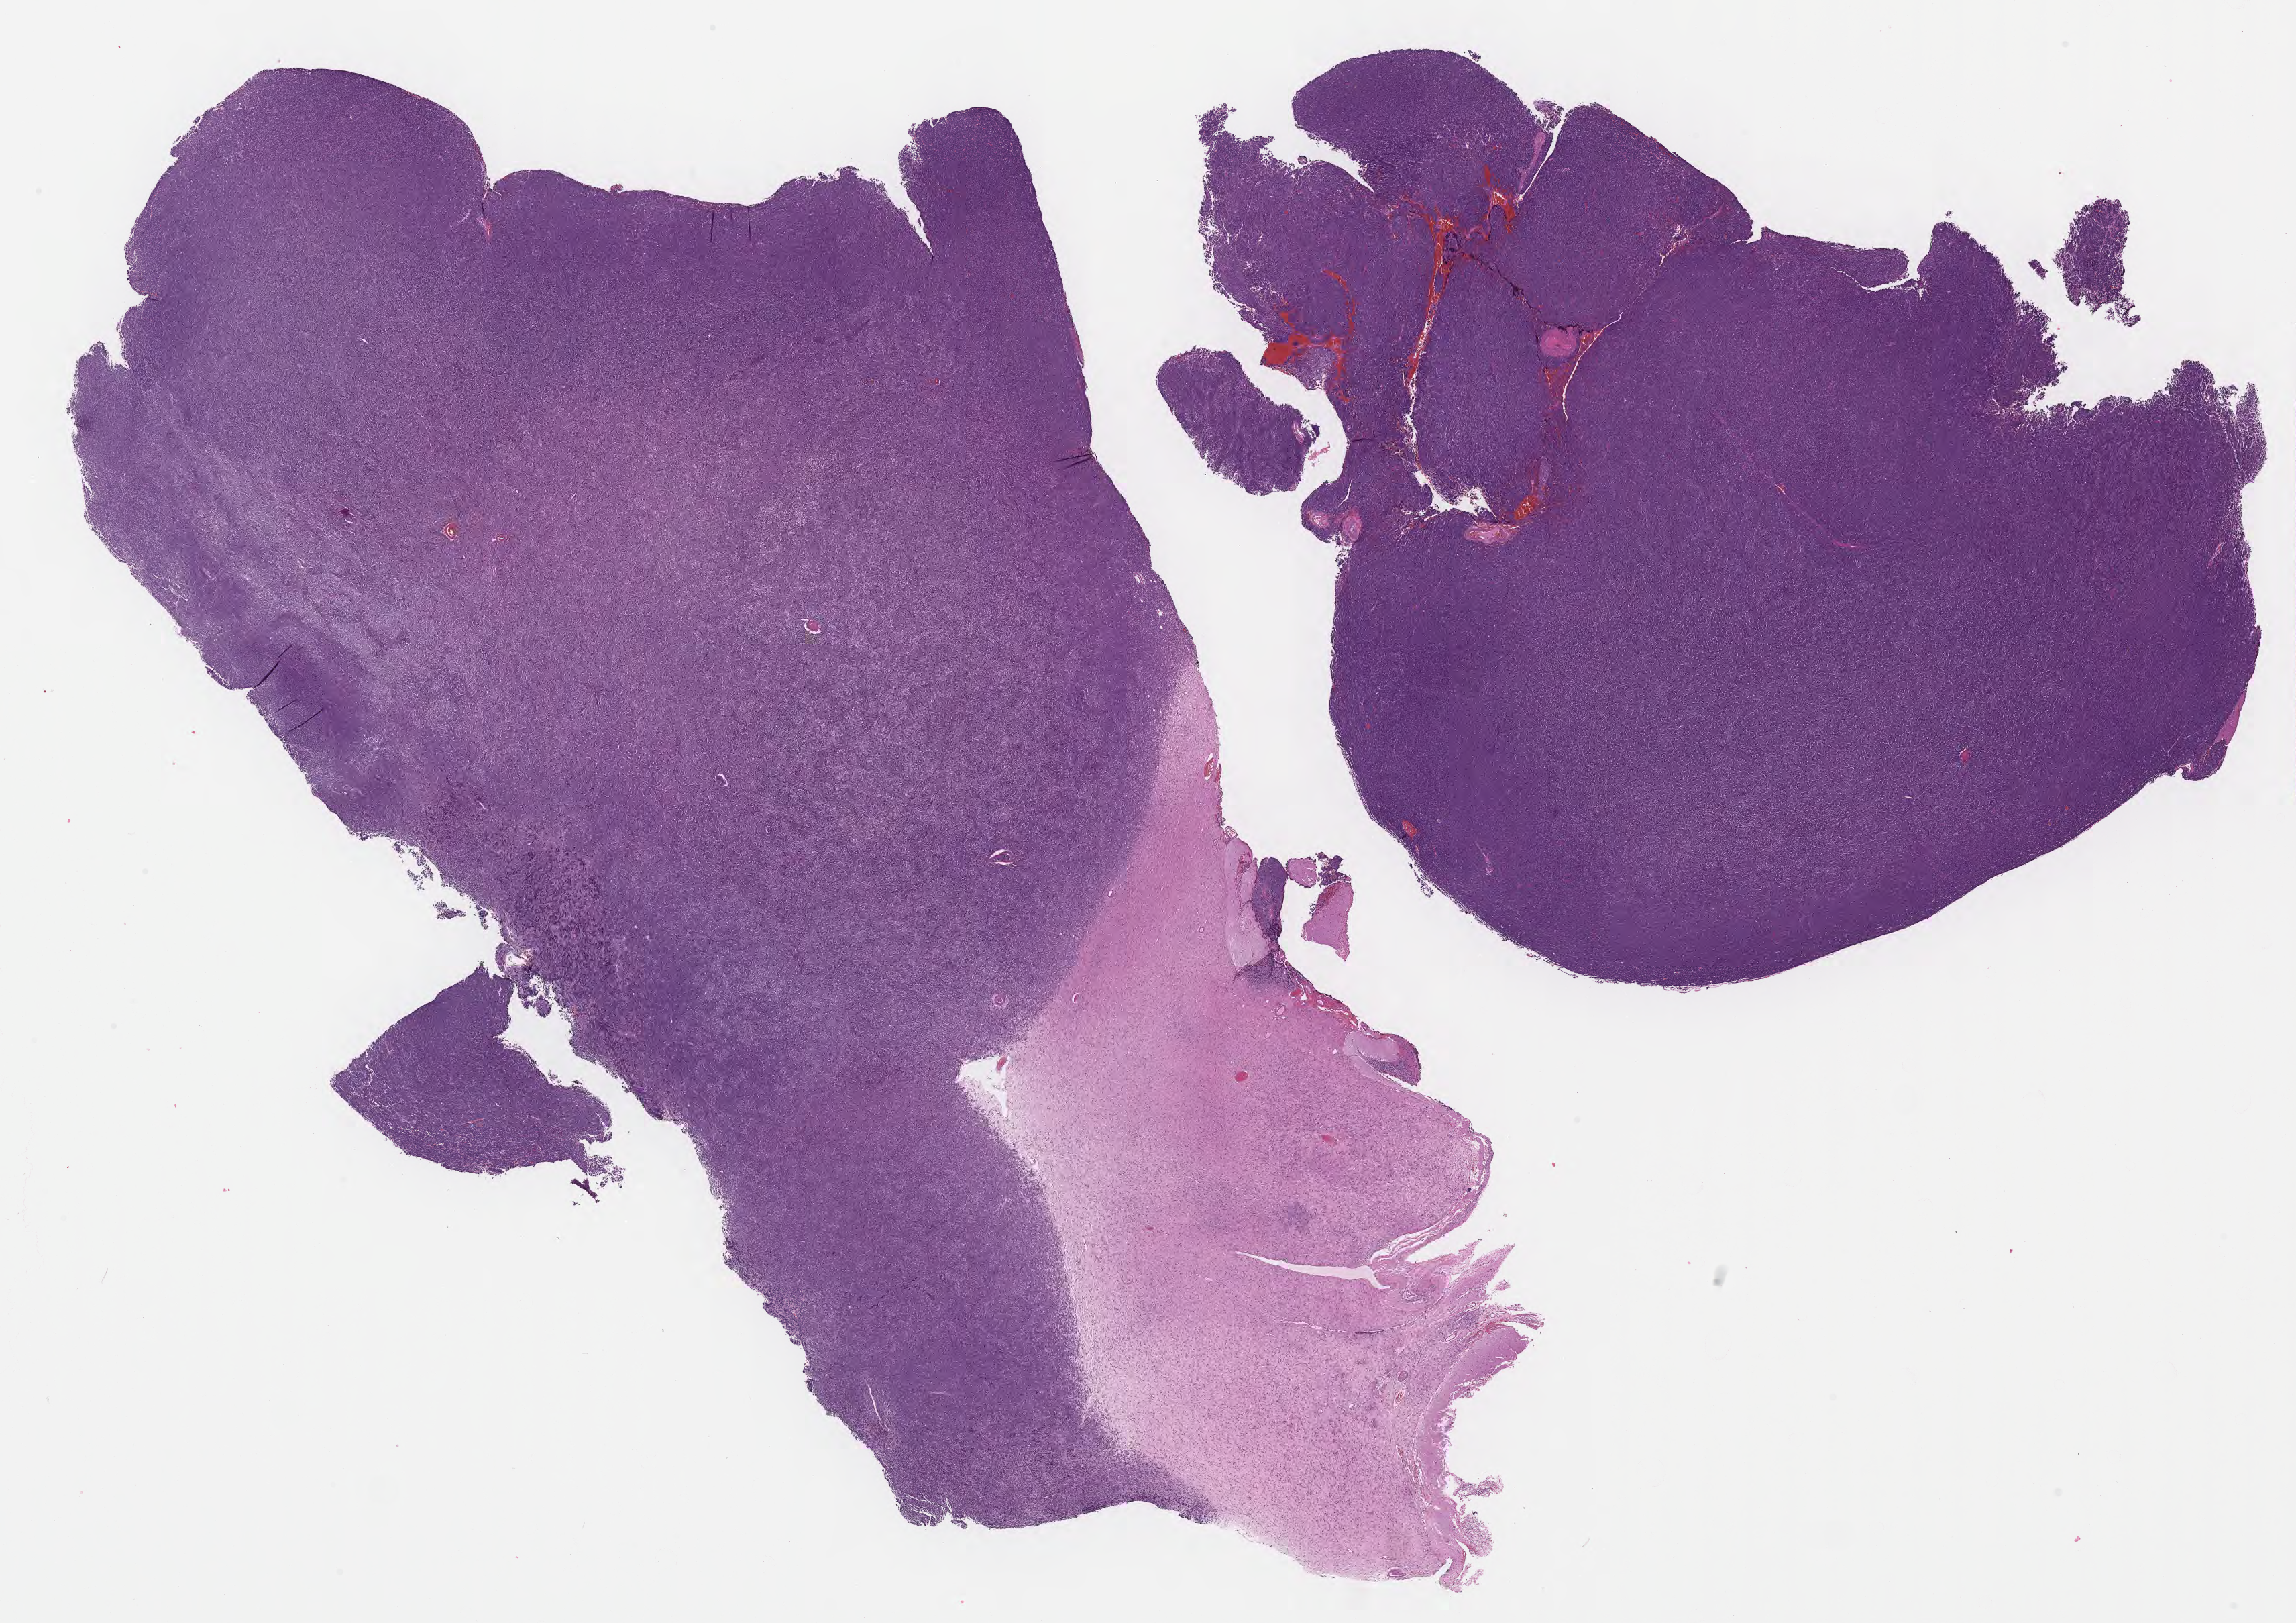
Digitized H&E-stained section of tumor tissue from the brain — shown as a low-resolution overview of the whole scanned area (about 27.7 x 19.6 mm); formalin-fixed, paraffin-embedded (FFPE) tissue. Female patient, age 54 months (4 years 6 months).
Diagnosis: Medulloblastoma, NOS.